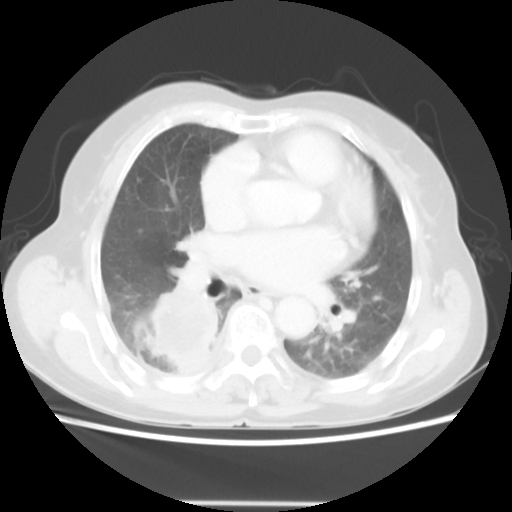
Chest CT, one axial slice; position 26 of 52 along the scan axis; 140 kVp; lung window (W 1500 / L -600 HU); 5 mm slice thickness; 512 × 512 image matrix, field of view 337 × 337 mm. Patient: female, 67 years. Case-level facts recorded for this patient, not image findings: clinical TNM (as recorded): T3 N1 M1.
Outlined on this slice (bounding box drawn by a radiologist):
- lung tumour (recorded histology: adenocarcinoma): bounding box <142,282,223,376> (left, top, right, bottom; pixels)